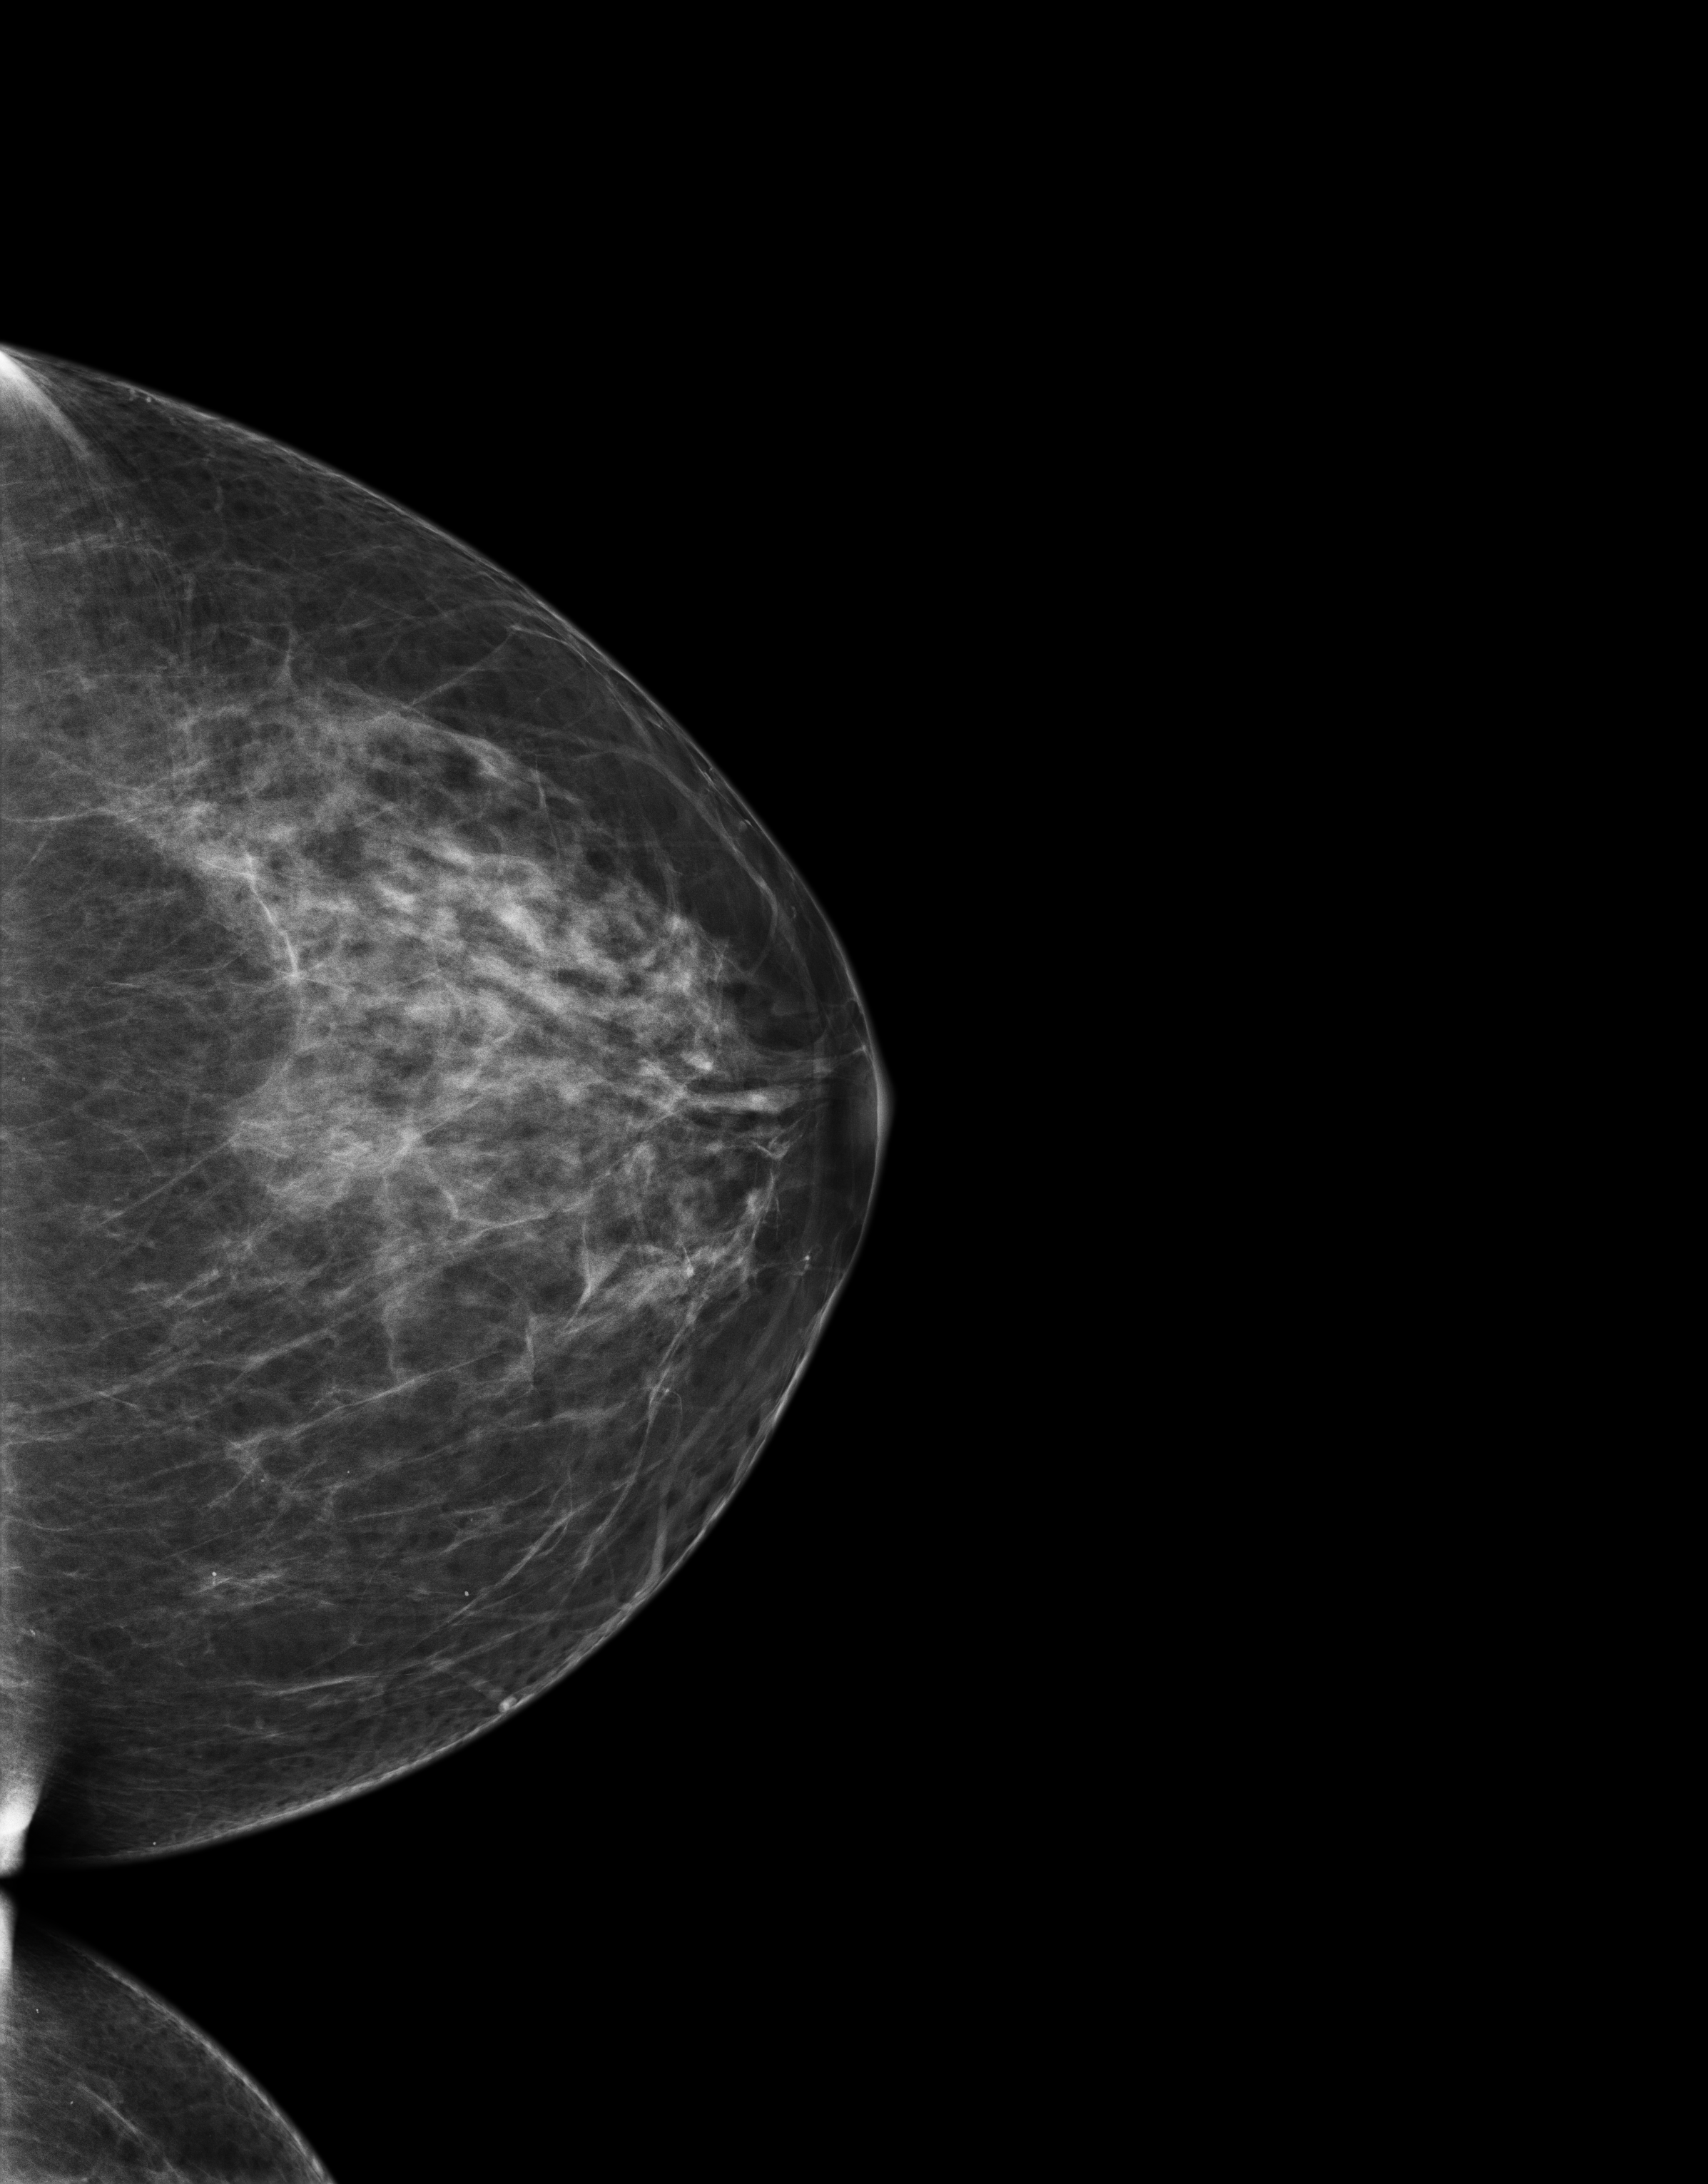
Digital mammogram (FFDM), left breast, cranio-caudal projection, annual screening mammography examination, compressed breast thickness 71 mm, system: Senographe Essential ADS_56.21.3. Patient: female, 57 years.
- BI-RADS breast density category at the screening exam (both breasts, scale 1–4): 2
- final BI-RADS assessment for this screening round (tomosynthesis exam, both breasts): category 1
- recall: no recall after this screen